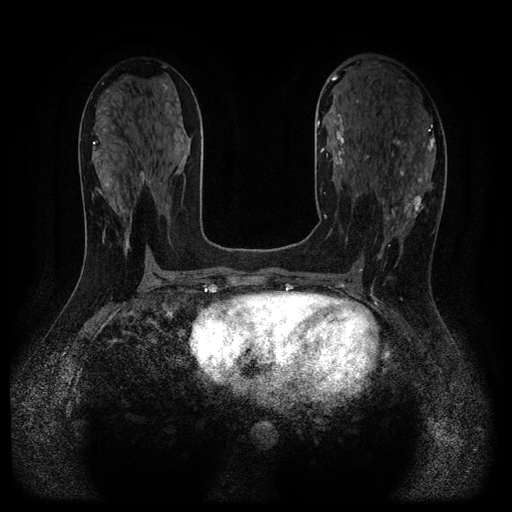
Breast MRI (dynamic contrast-enhanced, multi-phase), one axial slice. Position 55 of 116 along the scan axis. Dynamic contrast-enhanced series, time point 2 of 5 at this slice position (early post-contrast). 1.5 T. TE 2.7 ms, TR 5.4 ms. 2.2 mm slice thickness. 512 × 512 image matrix, field of view 330 × 330 mm. Female patient, age 43 years.
Structures marked on this image (semi-automatically segmented with operator editing):
- breast lesion (labelled 'tumour' in the annotation; benign lesions carry a separate 'benign' label): bounding box [x1, y1, x2, y2] px = [406, 192, 424, 218]
- breast lesion (labelled benign in the annotation): [321, 107, 345, 169]